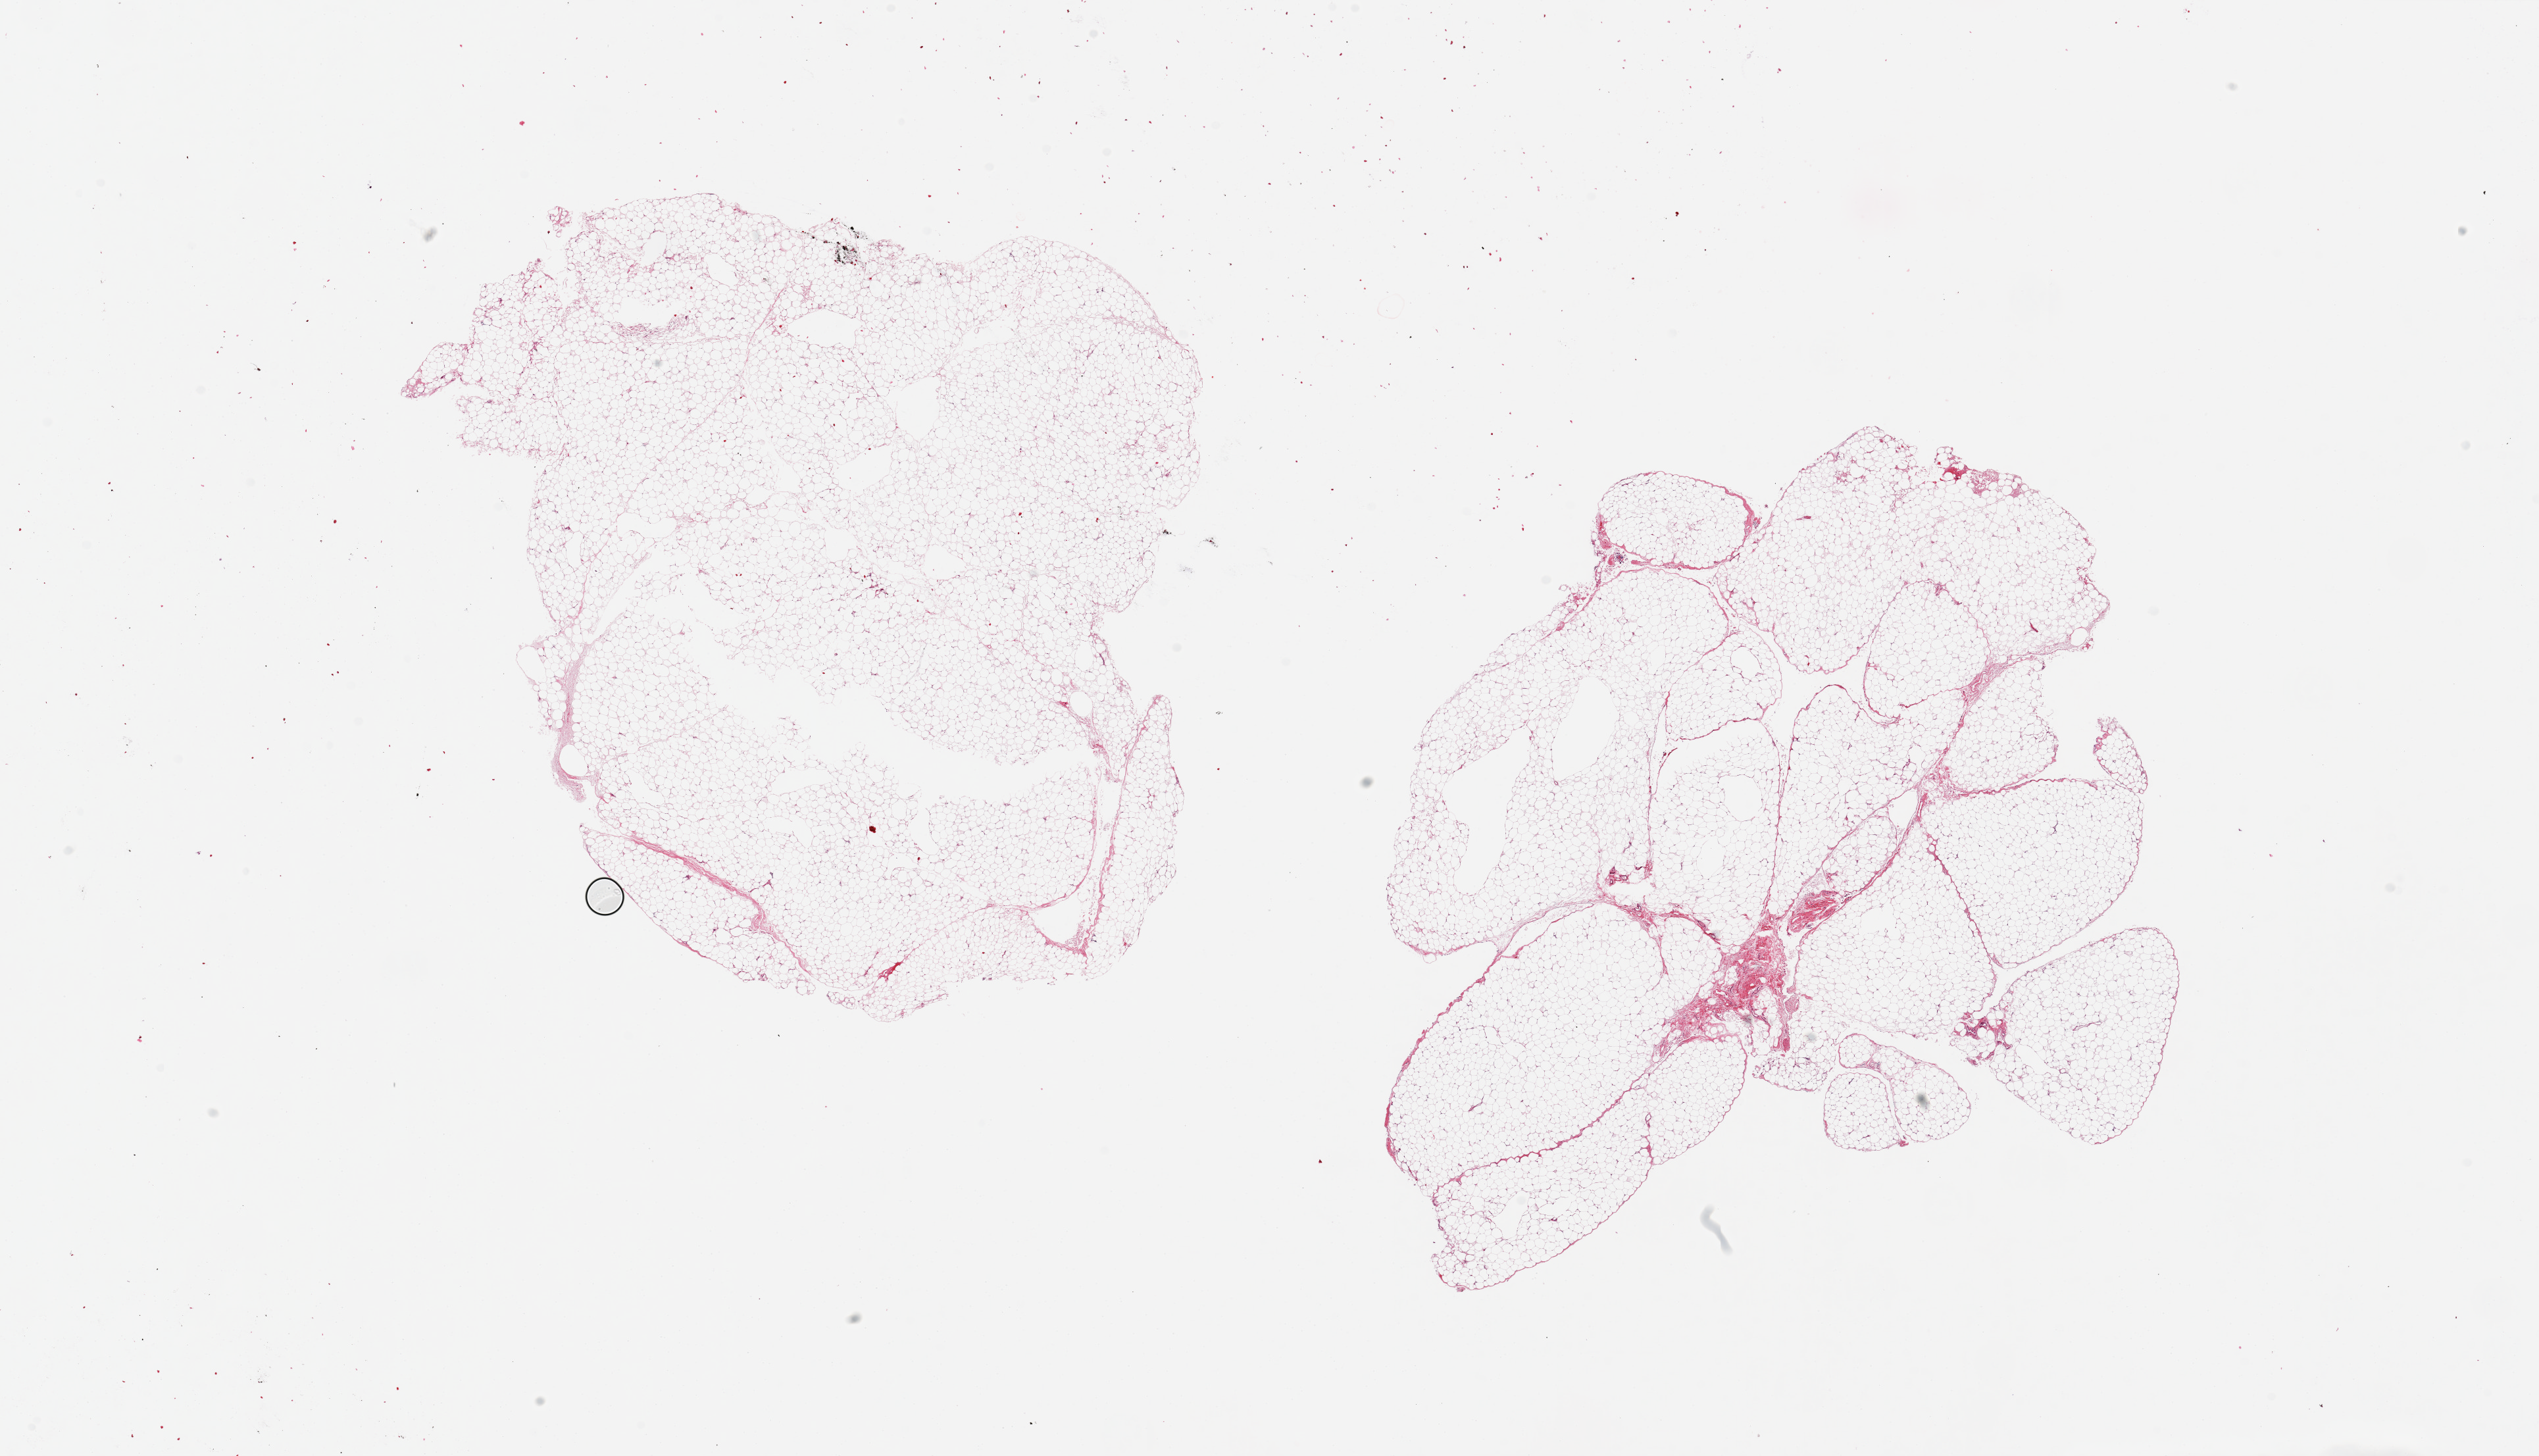
Hematoxylin and eosin (H&E) whole-slide image — a low-resolution overview of the entire scanned area, about 30.5 x 17.5 mm (acquisition: 20x scan); PAXgene-fixed paraffin-embedded (PFPE) section; target tissue: omentum; tissue donor sample. Male donor.
Review note (as recorded): 2 pieces ~9x8mm.